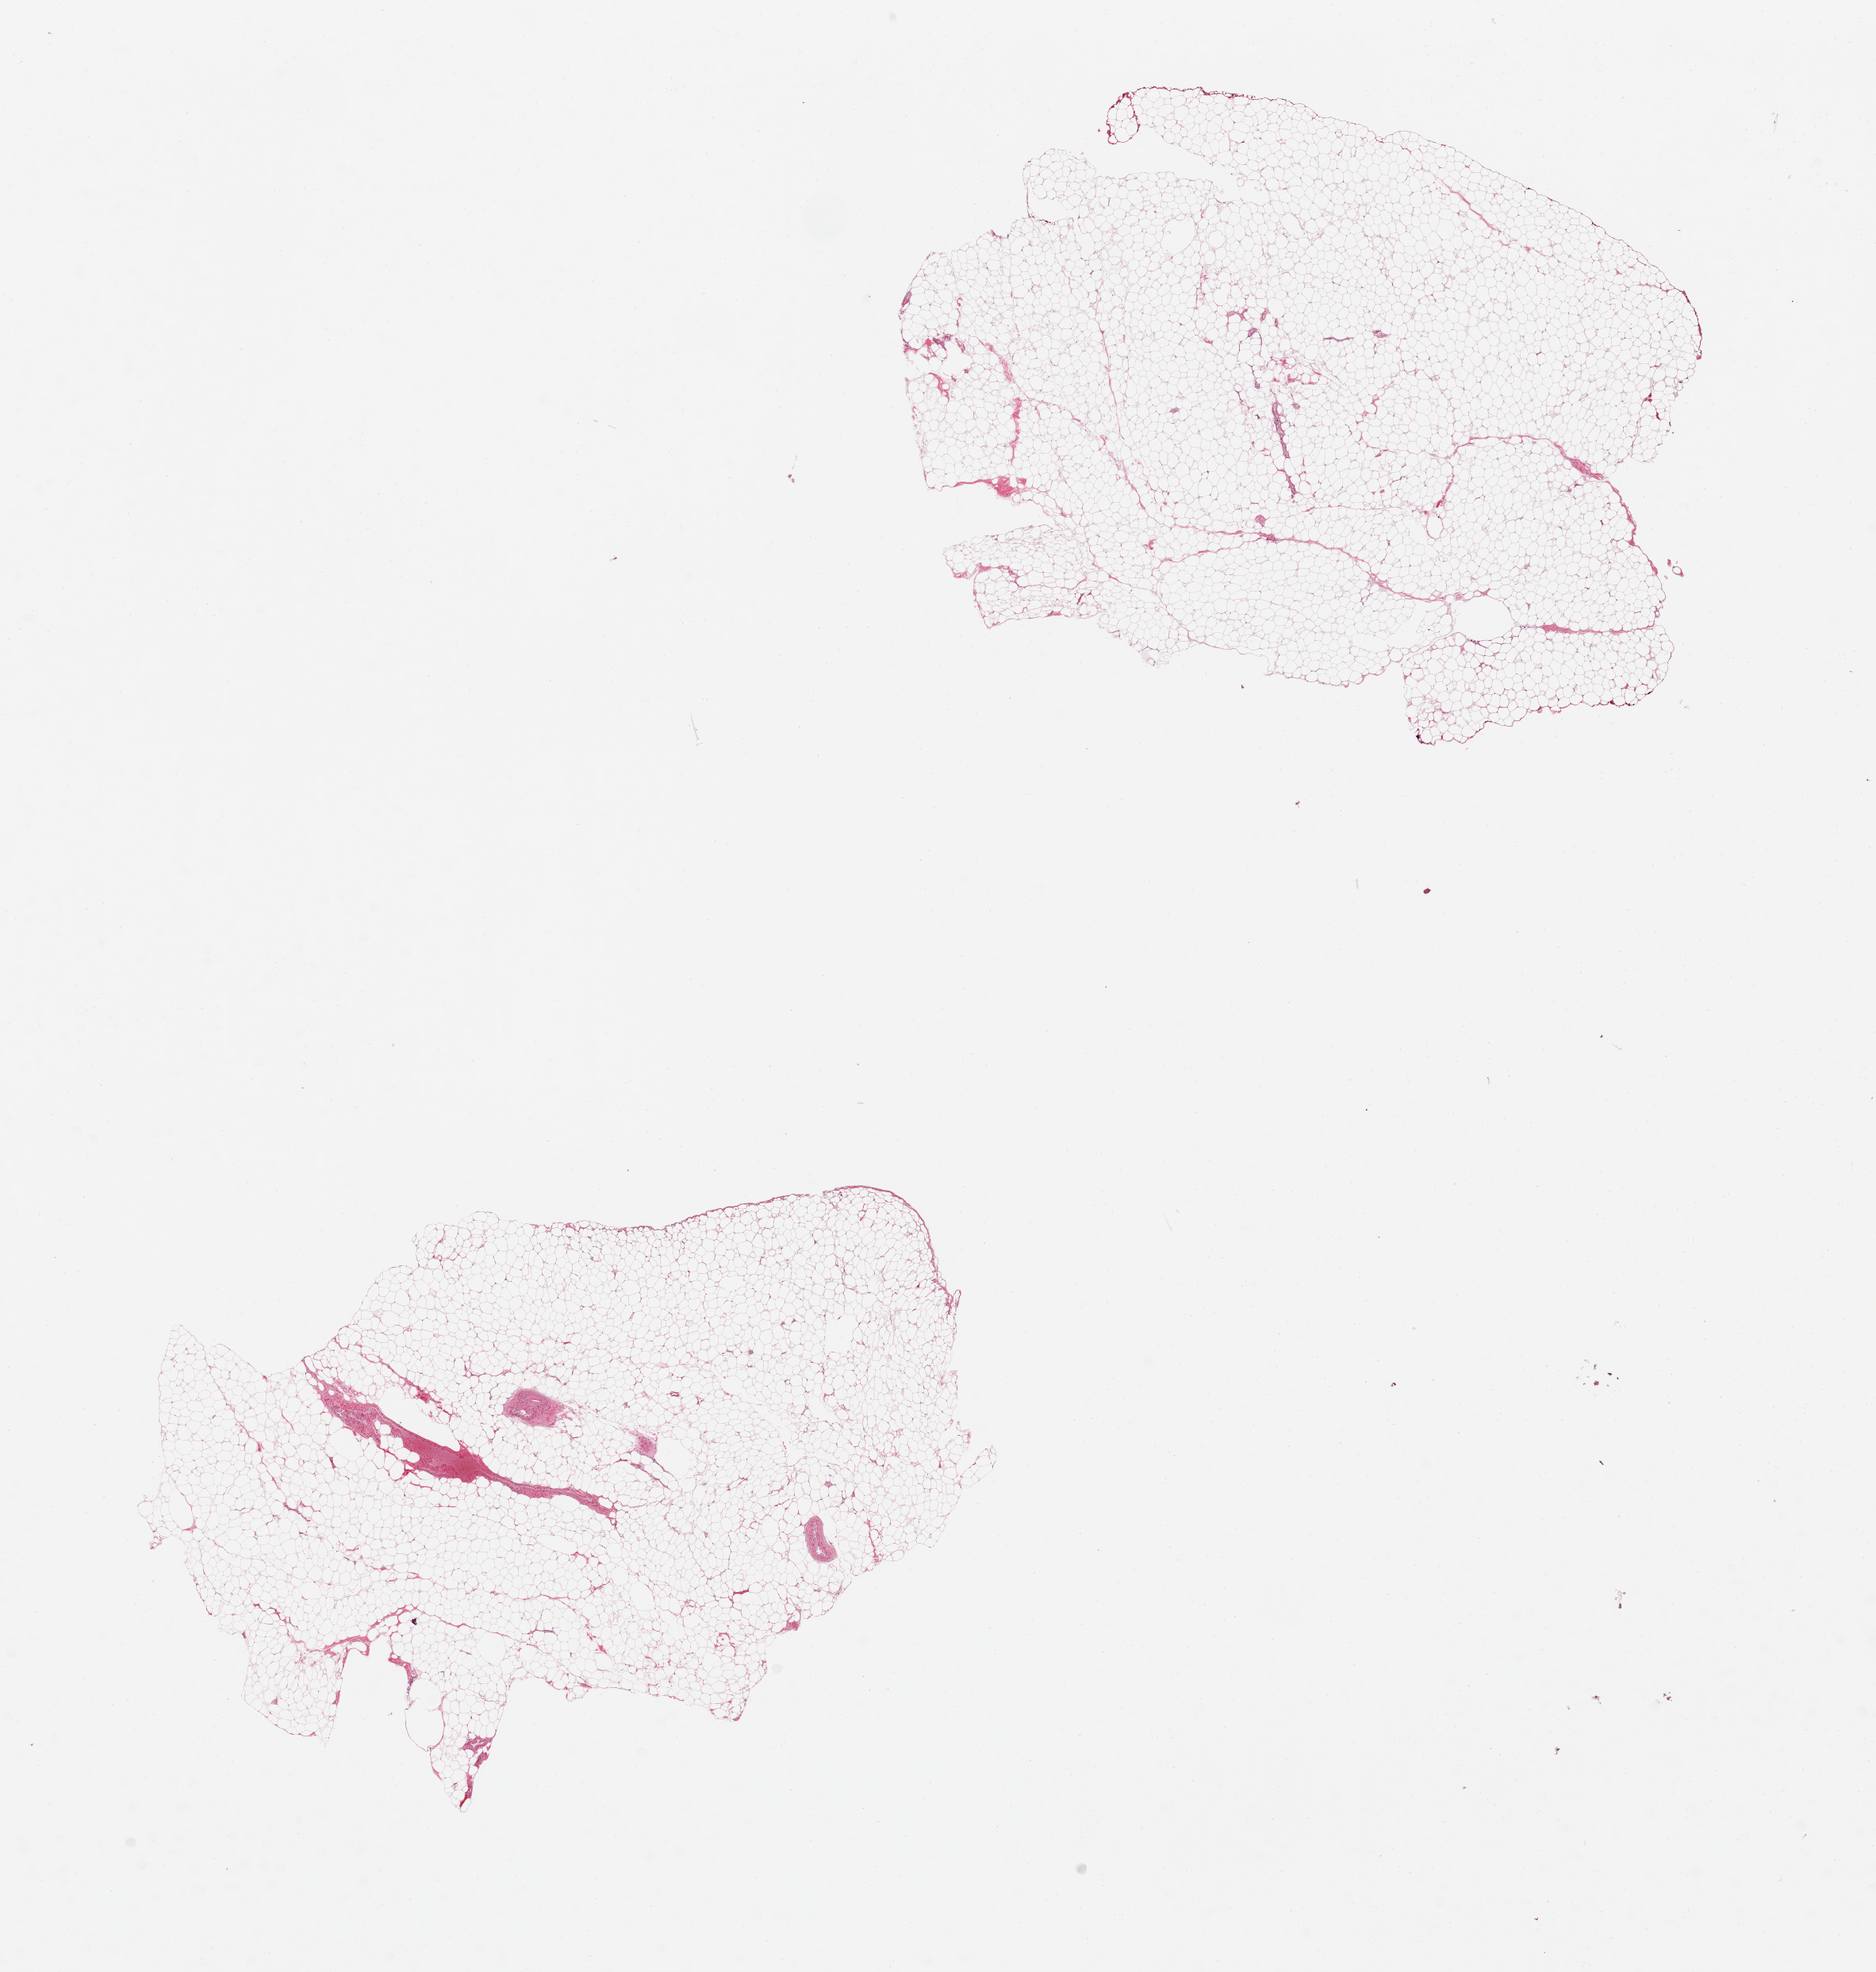
Whole-slide image, haematoxylin and eosin stain, brightfield — whole scanned area (about 18.7 x 19.7 mm) shown as a low-resolution overview; PAXgene-fixed paraffin-embedded (PFPE) section; section of omentum (target tissue); donor tissue sample. Female donor.
Review note (as recorded): 2 pieces, minimal fibrous tissue.